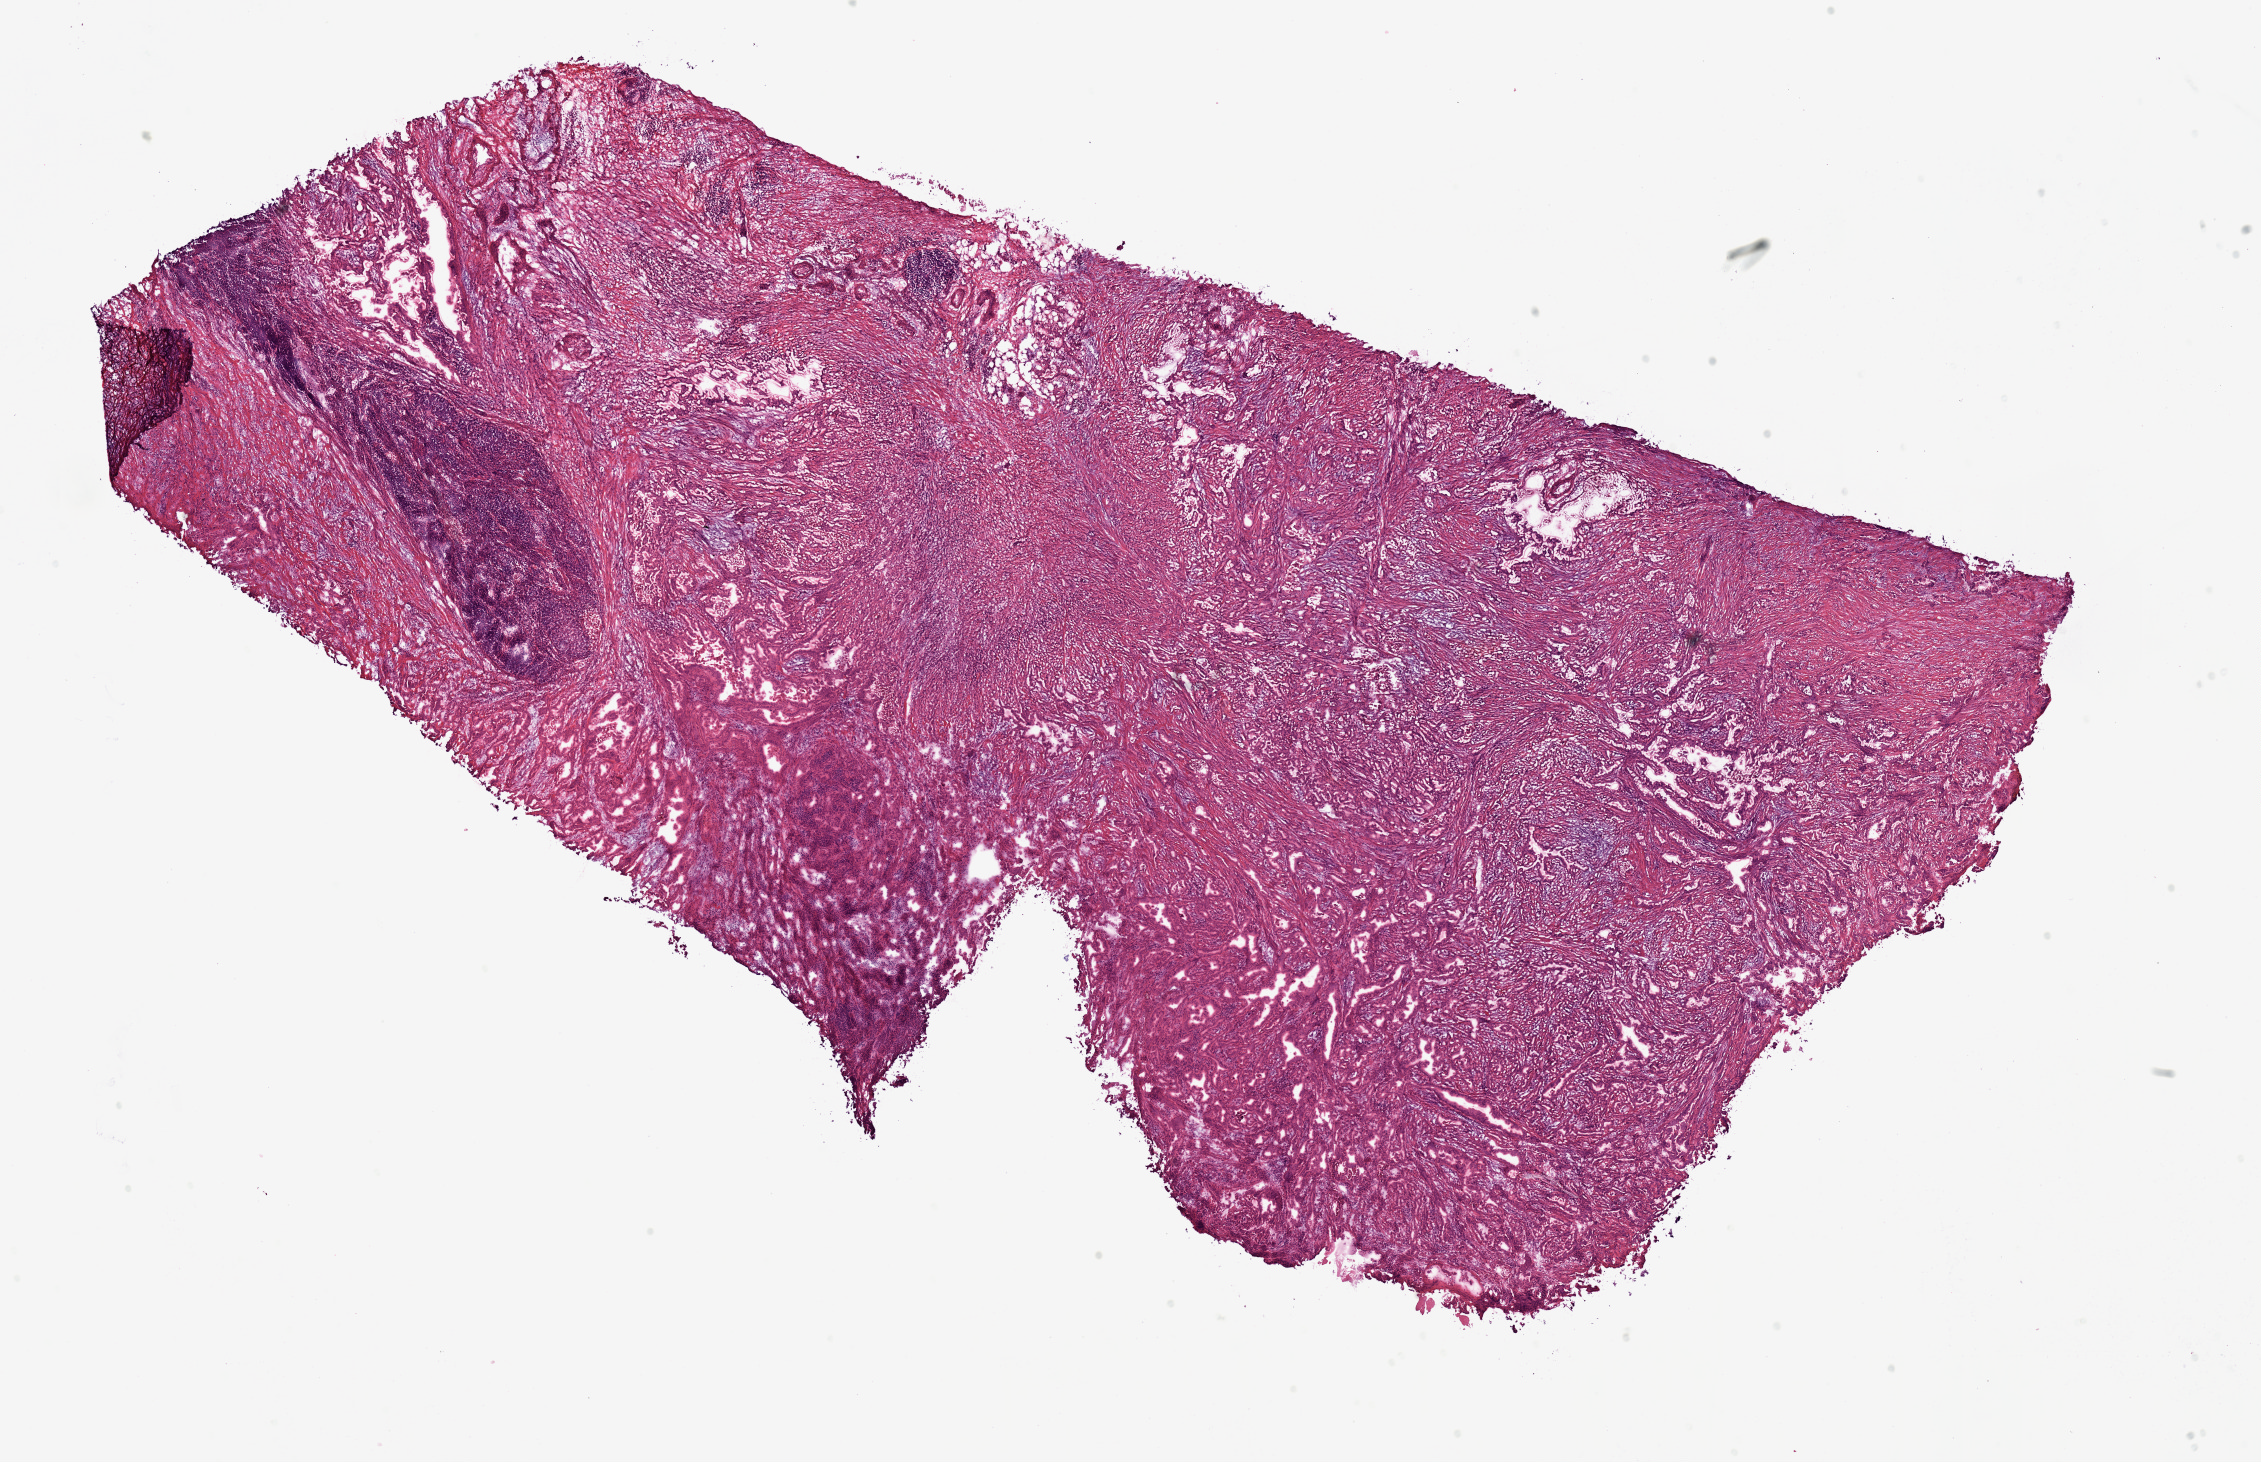
Whole-slide histology image, Hematoxylin and eosin (H&E) stained — a low-resolution overview of the entire scanned area, about 17.9 x 11.6 mm (from a 20x scan), frozen section from the top of the tissue portion, stomach, primary tumour sample. Male patient; age at initial diagnosis 58 years. Histologic grade: G2 (moderately differentiated). Pathologist review of this section (percent, as recorded): tumour cells 80%, tumour nuclei 75%, normal cells 0%, stromal cells 20%, necrosis 0%.
AJCC pathologic stage: II (6th edition). Histologic diagnosis: Adenocarcinoma, NOS.